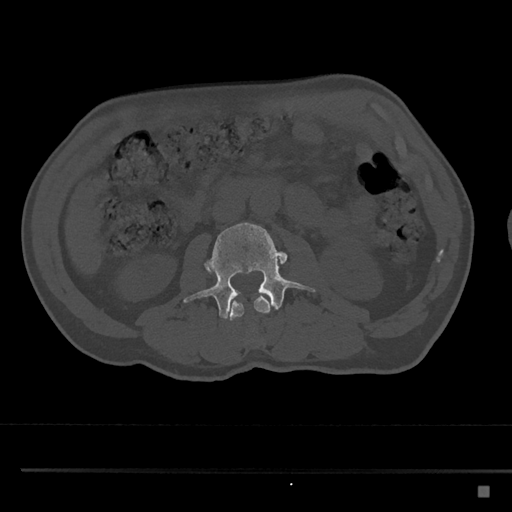
CT including the spine, one axial slice. Position 715 of 797 along the scan axis. Reconstruction kernel Br40s/3. Bone window (W 1800 / L 400 HU). 0.5 mm slice thickness. 512 × 512 image matrix, field of view 391 × 391 mm. Patient: male, 59 years. From the clinical record (not read from this slice): primary cancer: prostate.
Structures marked on this image (semi-automatic segmentation, software-assisted and operator-edited):
- L2 vertebra: bounding box <229,295,271,321> (left, top, right, bottom; pixels)
- L3 vertebra: <183,222,316,319>